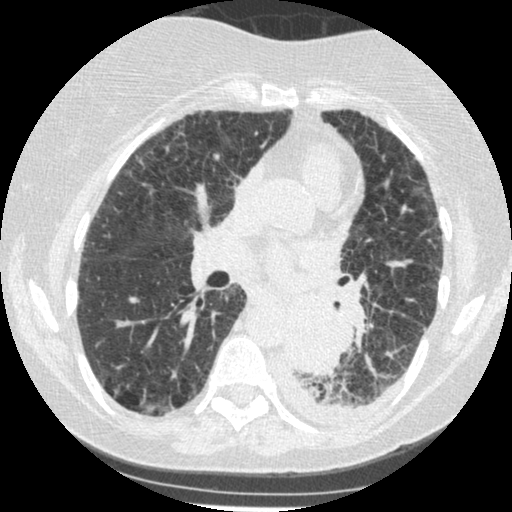
Axial slice from a low-dose chest CT screening exam; third screening round (two years after baseline); lung window (W 1500 / L -600 HU); 1.25 mm slice thickness; 512 × 512 image matrix, field of view 310 × 310 mm. Female, age 60 years at enrolment. Former smoker at enrolment.
• Expert-annotated lung lesion, bounding box [x1, y1, x2, y2] px = [272, 306, 342, 375].
• Reader record for this screening exam (exam-level; its link to the box is not recorded): non-calcified nodule or mass ≥4 mm, left lower lobe, 54 × 38 mm, smooth margins, soft tissue attenuation, pre-existing on the prior screen: yes; interval growth: yes.
• Participant outcome: lung cancer diagnosed 15 days after this screen — small cell carcinoma, NOS, left lower lobe, undifferentiated (G4), stage IV (AJCC 6th edition), 69 mm at pathology.